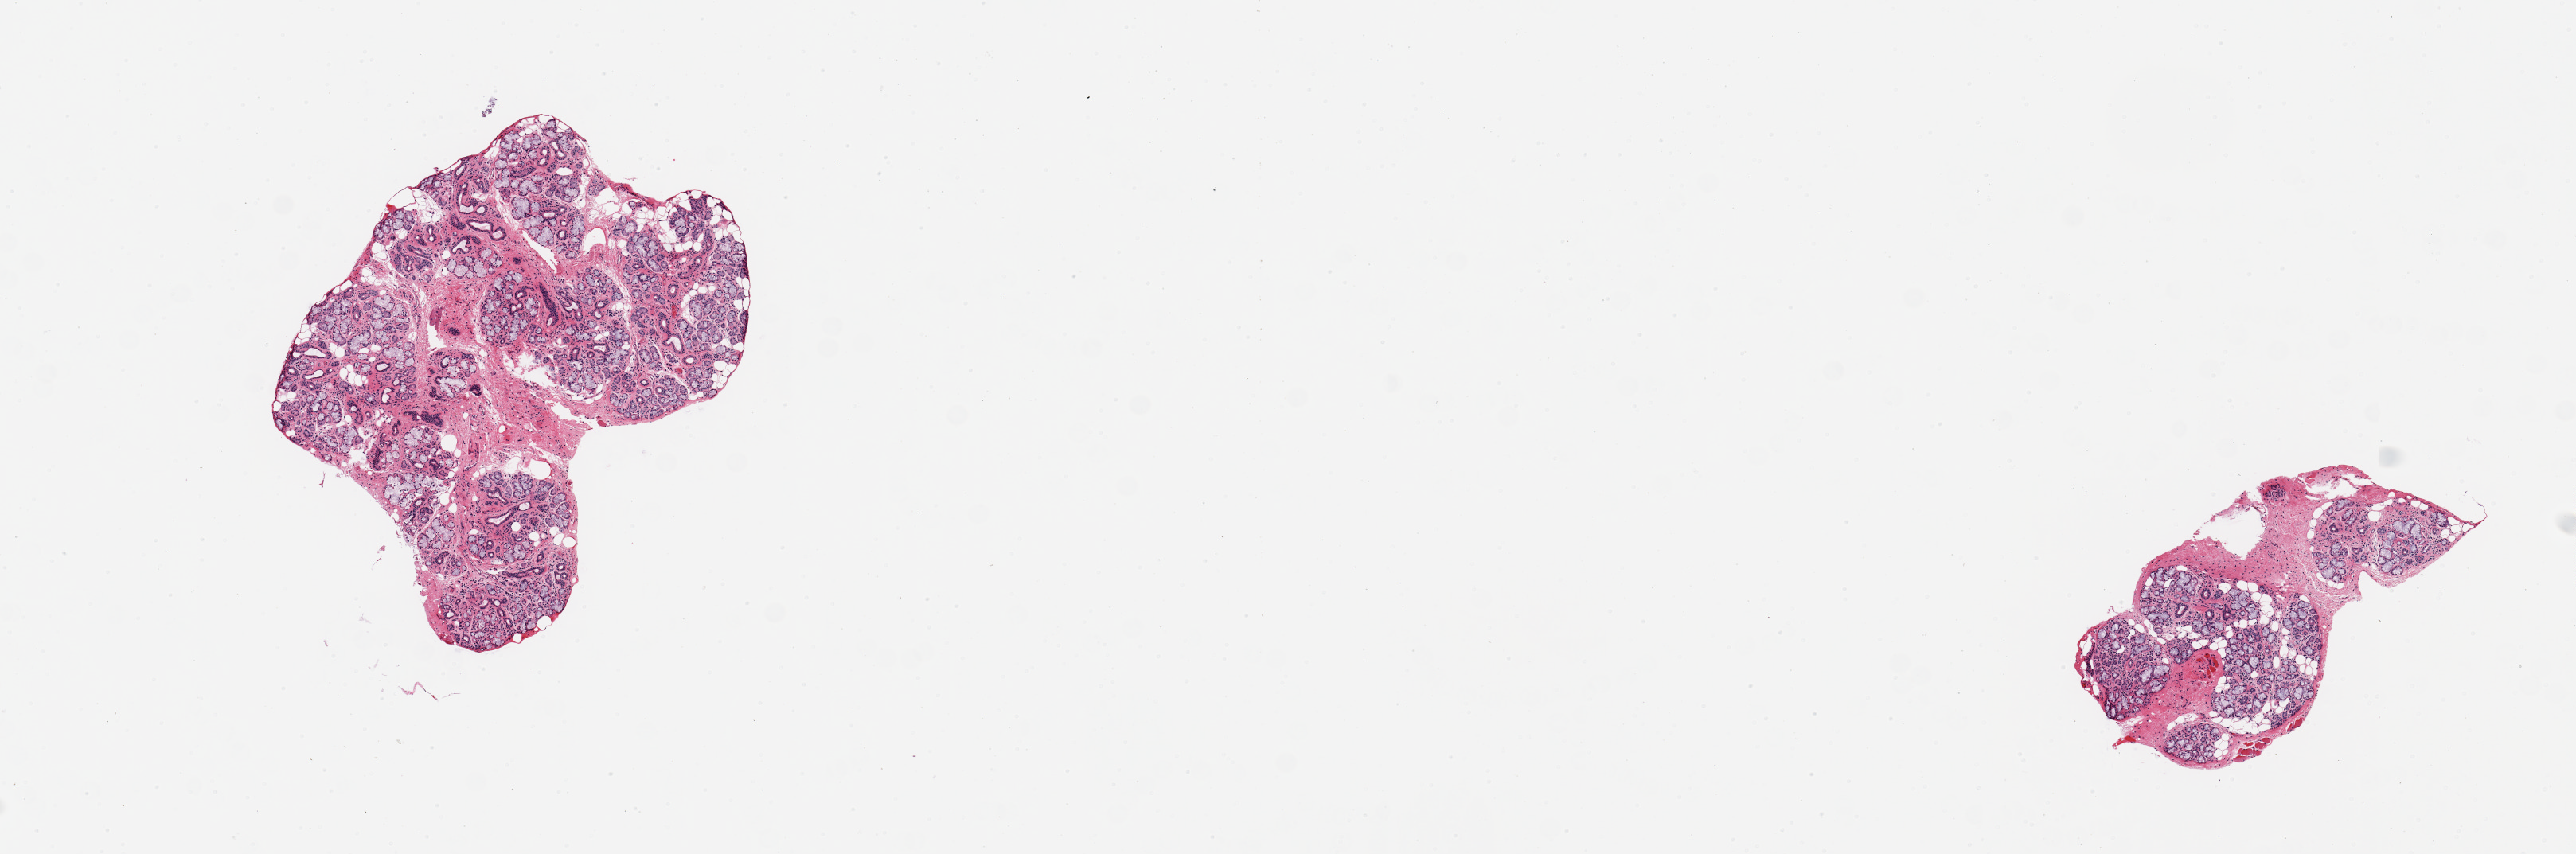
Digitized hematoxylin and eosin (H&E)-stained section — whole scanned area (about 12.8 x 4.2 mm) shown as a low-resolution overview; PAXgene-fixed paraffin-embedded (PFPE) section; sampled site (target tissue): minor salivary gland; tissue donor sample. Male donor.
Pathologist's review note for this sample: 2 pieces; well dissected glands with 10% internal fat.